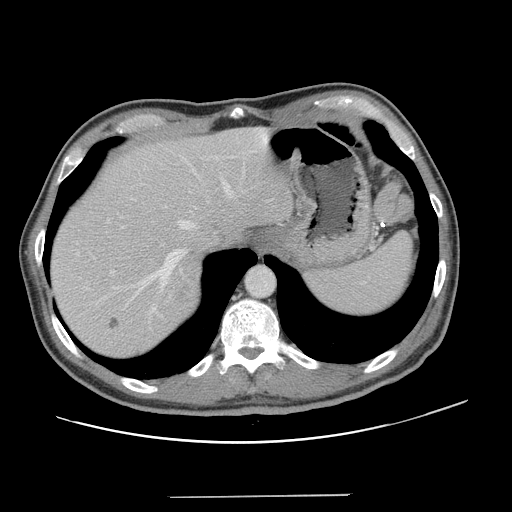
Contrast-enhanced abdominal CT, one axial slice; slice 106 of 131 in the series (ordered by position); 120 kVp; intravenous contrast given; soft-tissue window (W 400 / L 40 HU); 2.5 mm slice thickness; 512 × 512 image matrix, field of view 403 × 403 mm. Male patient, age 60 years. From the clinical record (not read from this slice): diagnosis: colorectal cancer liver metastases, imaged before liver resection; multiple liver metastases: no; largest metastasis: 2.5 cm; chemotherapy before resection: no.
Structures marked on this image (outlined manually by an expert reader):
- hepatic veins: bounding box <122,158,231,312> (left, top, right, bottom; pixels)
- liver: <50,126,294,358>
- planned liver remnant (the part of the liver to remain after resection): <50,126,294,348>
- portal vein (with intrahepatic branches): <93,155,233,275>
- liver metastasis: <175,289,190,303>